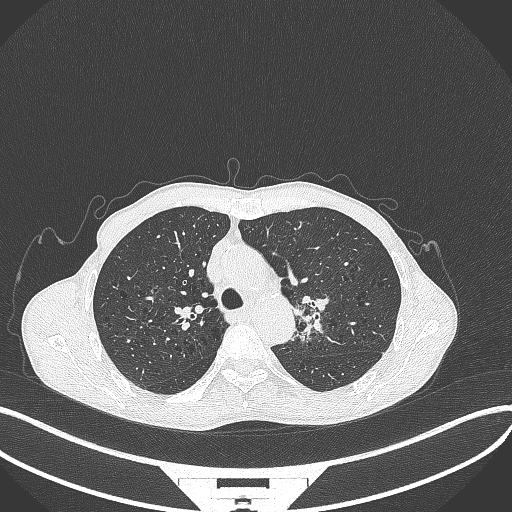
Chest CT, one axial slice; slice 302 of 386 in the series (ordered by position); reconstruction kernel B70f; 120 kVp; lung window (W 1500 / L -600 HU); 512 × 512 image matrix, field of view 400 × 400 mm. Male patient, age 65 years. From the clinical record (not read from this slice): clinical TNM (as recorded): T2b N0 M0; histopathological grade: G2.
Annotated regions visible in this slice (bounding box drawn by a radiologist):
- lung tumour (recorded histology: adenocarcinoma): bounding box (x1, y1, x2, y2) in pixels: (290, 285, 330, 345)